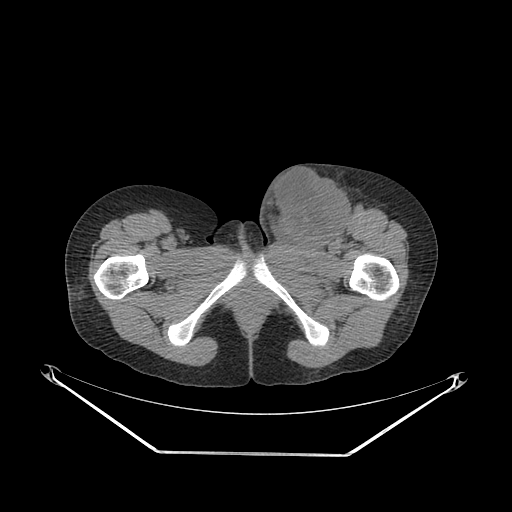
CT of an extremity soft-tissue mass (from a PET/CT study), one axial slice. Reconstruction kernel SOFT. 140 kVp. Soft-tissue window (W 400 / L 40 HU). 512 × 512 image matrix, field of view 500 × 500 mm. Female patient. From the clinical record (not read from this slice): histological type: leiomyosarcoma; grade: high; site of the primary tumour: groin.
Annotated regions visible in this slice (expert contour drawn on MRI and transferred to this co-registered scan by the dataset authors):
- gross tumour volume including surrounding oedema: bounding box [x1, y1, x2, y2] px = [256, 164, 366, 248]
- gross tumour volume (mass): [265, 169, 348, 245]